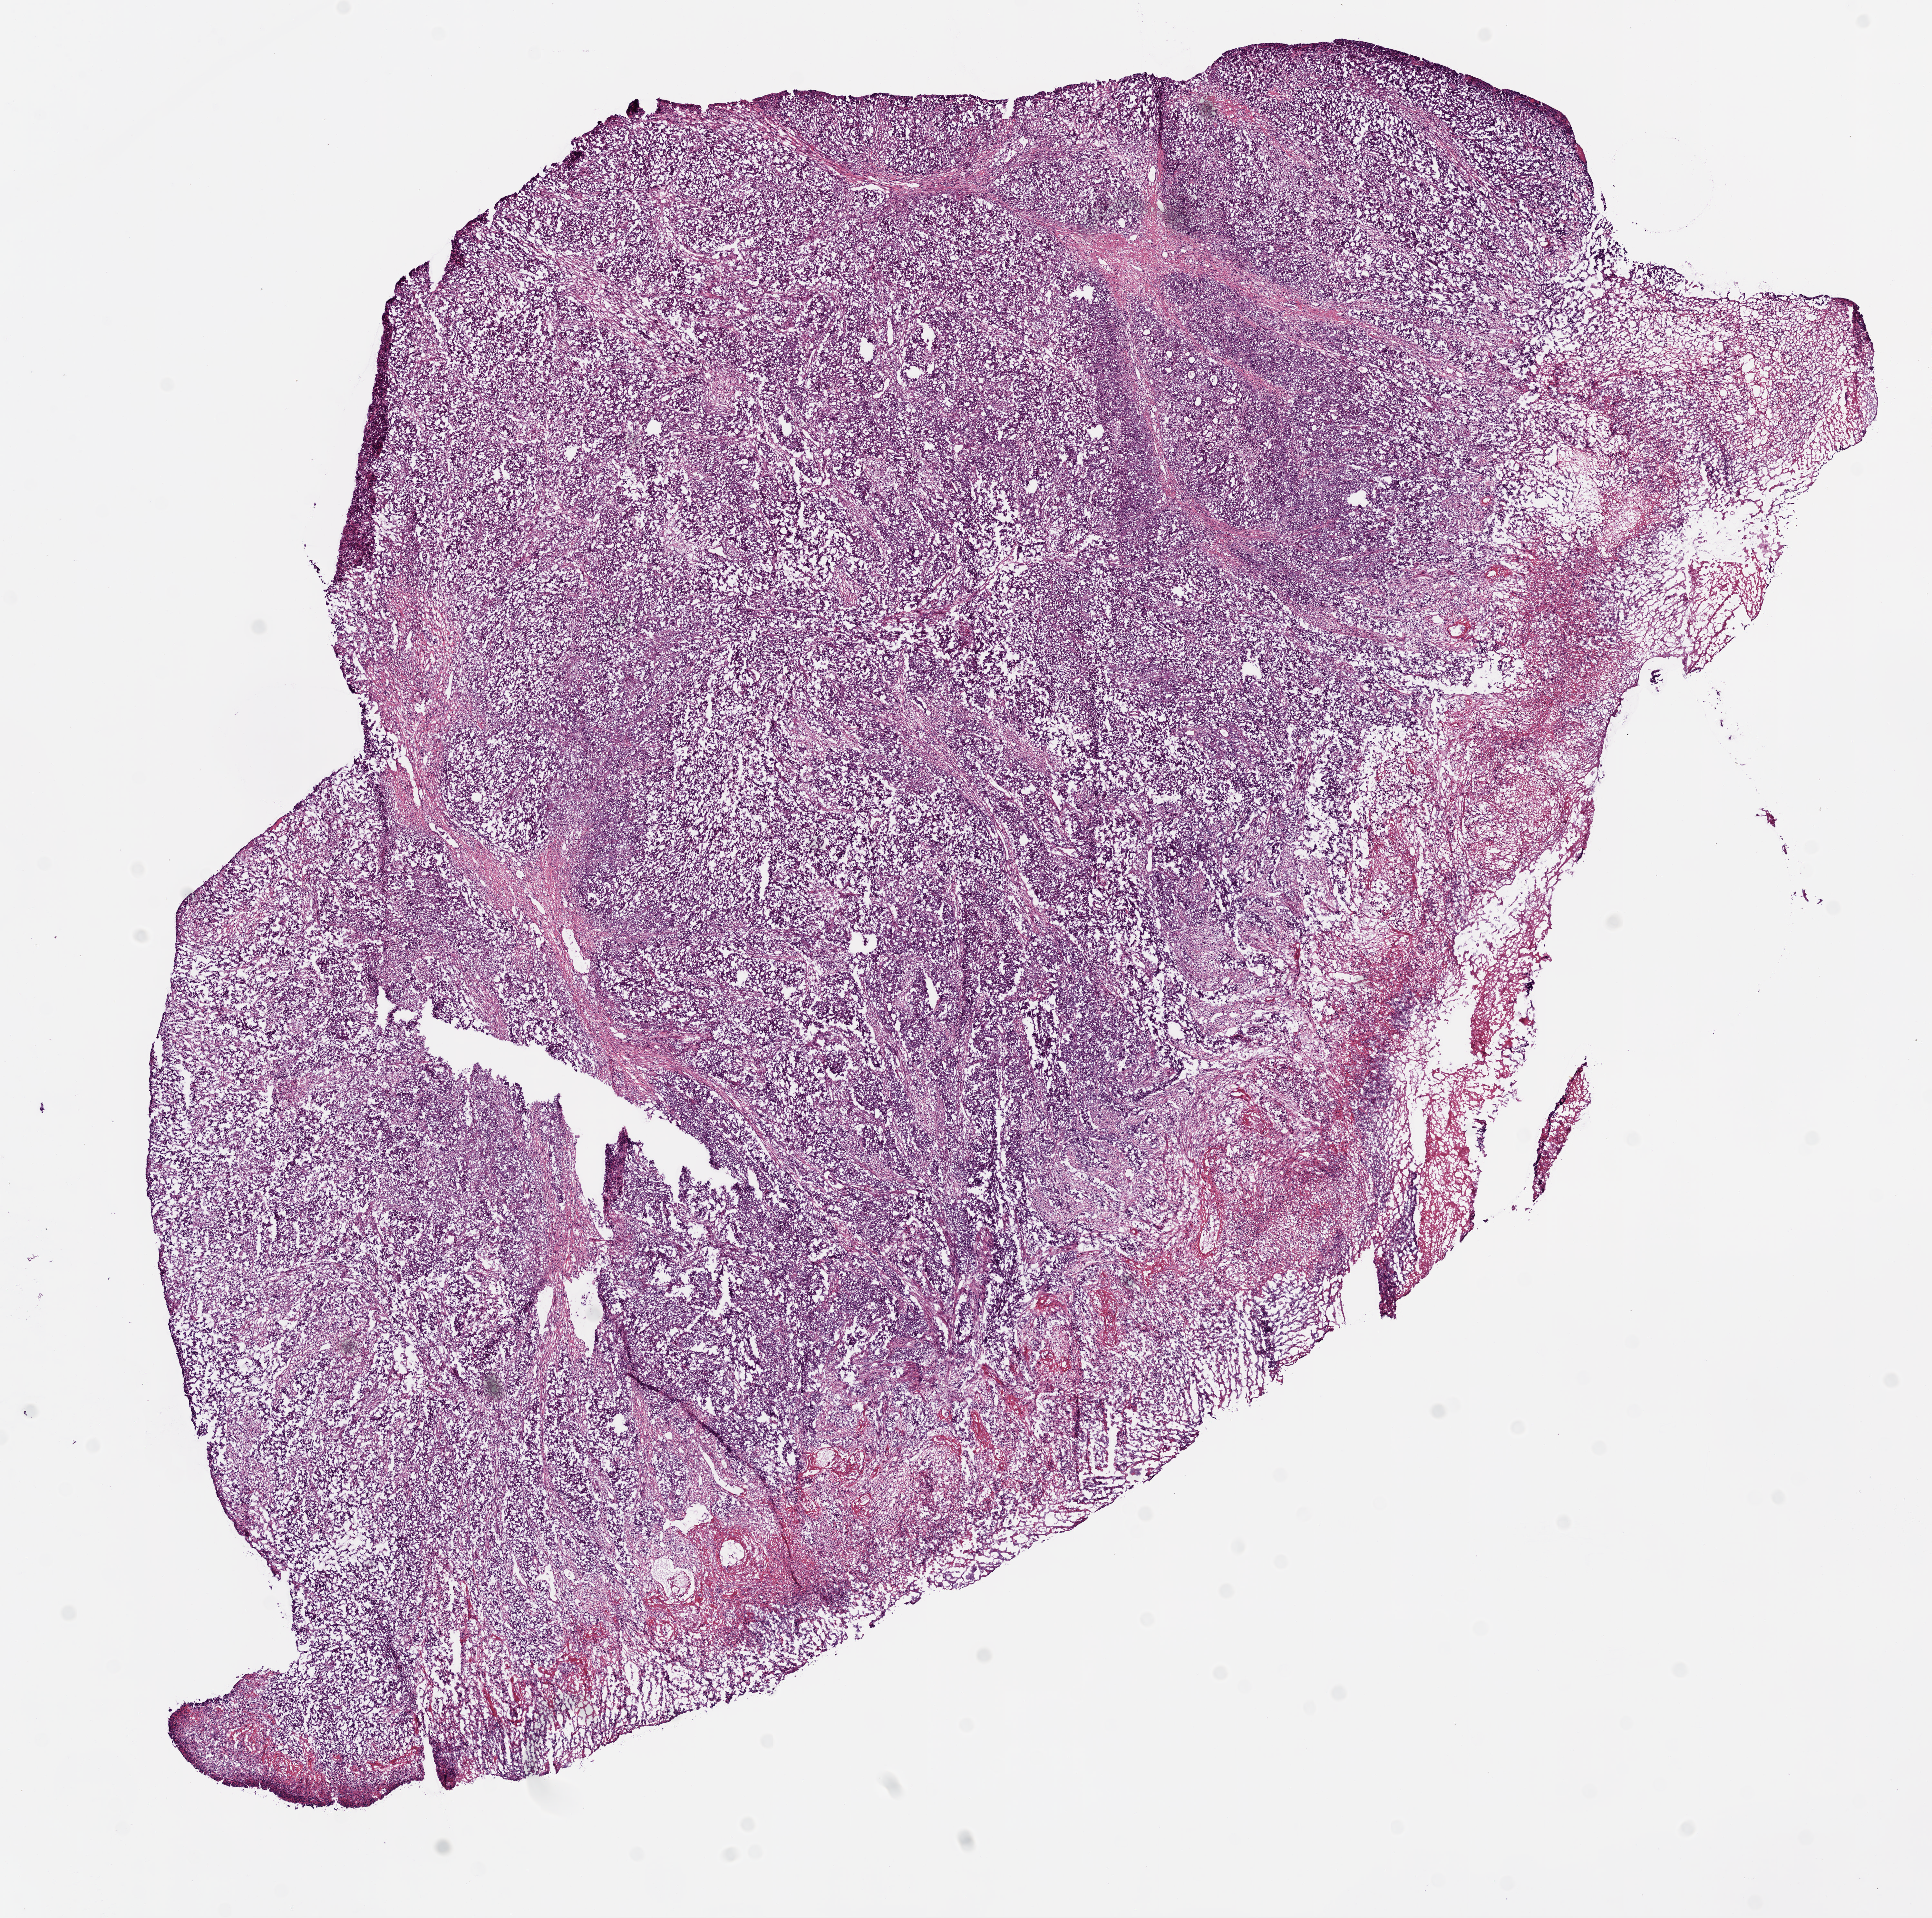
H&E whole-slide image — whole scanned area (about 12.1 x 12.0 mm, slide scanned at 20x) shown as a low-resolution overview, frozen section, stomach, primary tumour sample. Male, age 62 years at initial diagnosis. Histologic grade: G3 (poorly differentiated). Slide review estimates, as recorded: tumour cells 80%, tumour nuclei 80%, normal cells 0%, stromal cells 10%, necrosis 0%.
Pathologic diagnosis: Carcinoma, diffuse type. AJCC pathologic stage: IB (7th edition).